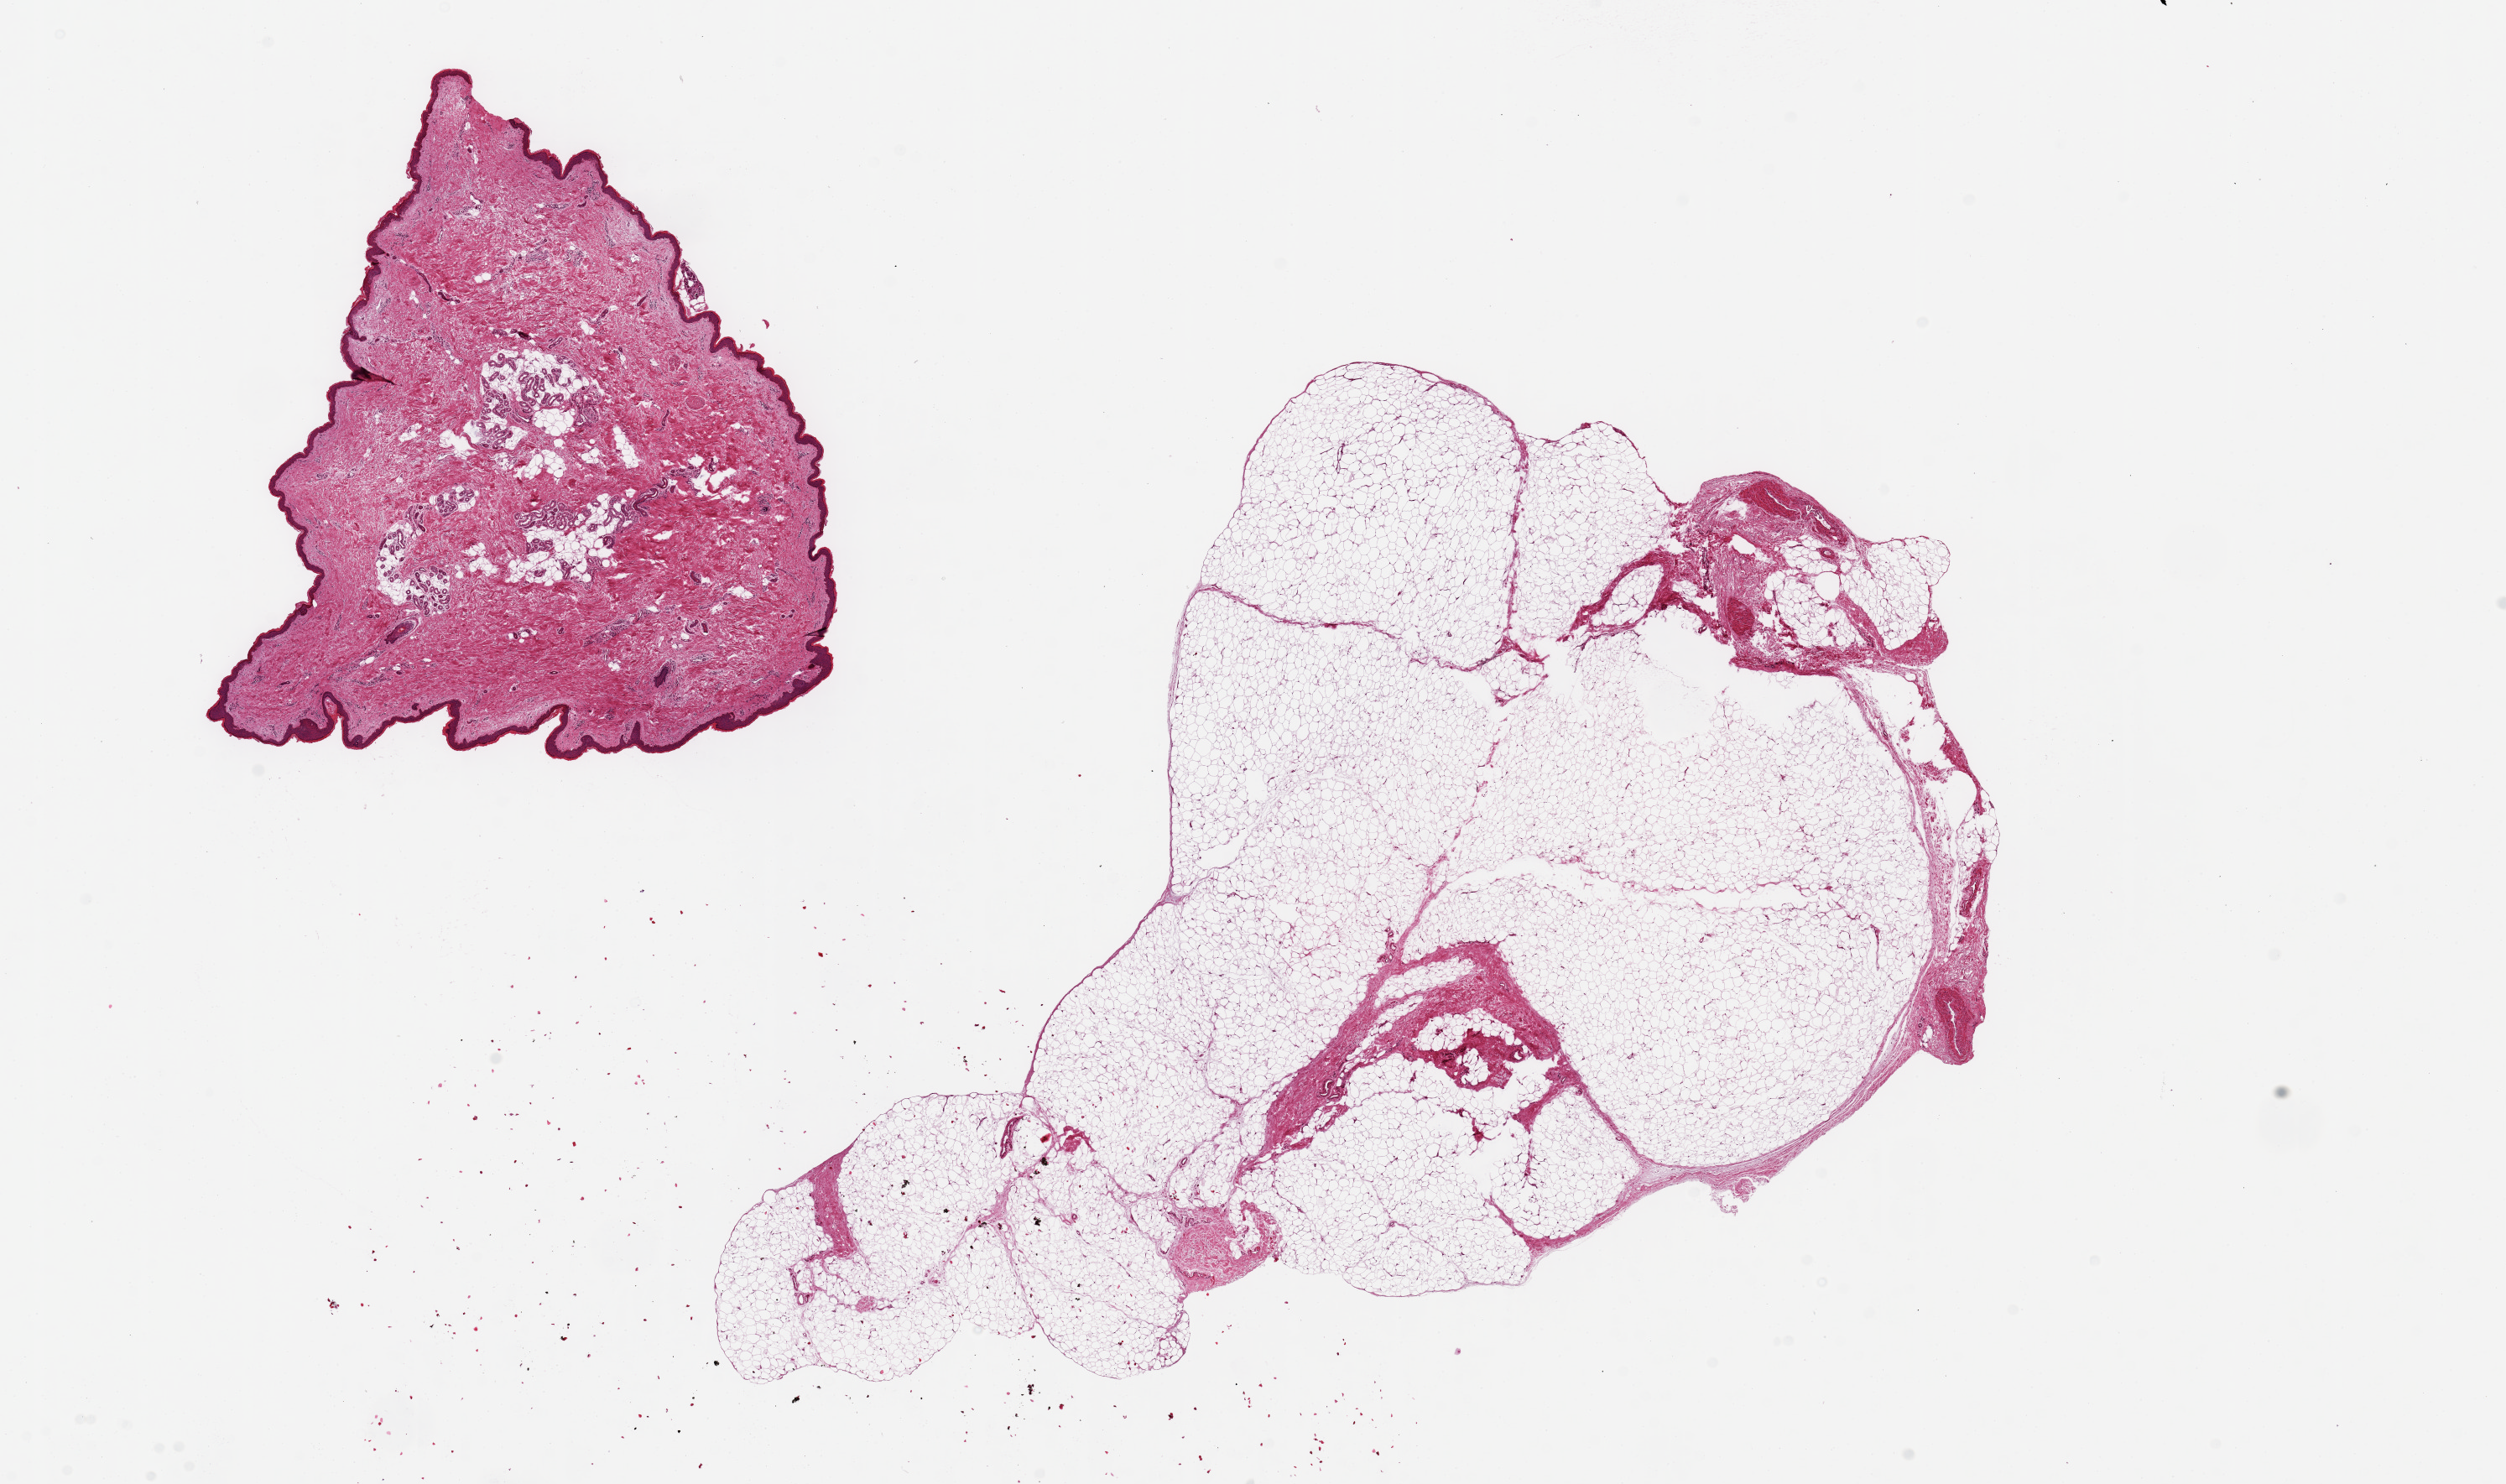
Whole-slide image, haematoxylin and eosin stain — low-resolution overview of the scanned area, about 23.6 x 14.0 mm, PAXgene-fixed paraffin-embedded (PFPE) section, target tissue: adipose tissue, tissue donor sample. Male donor.
Pathologist's review note for this sample: 2 pieces, 7x6 & 14x9mm; Larger piece is adipose tissue, smaller piece is skin.